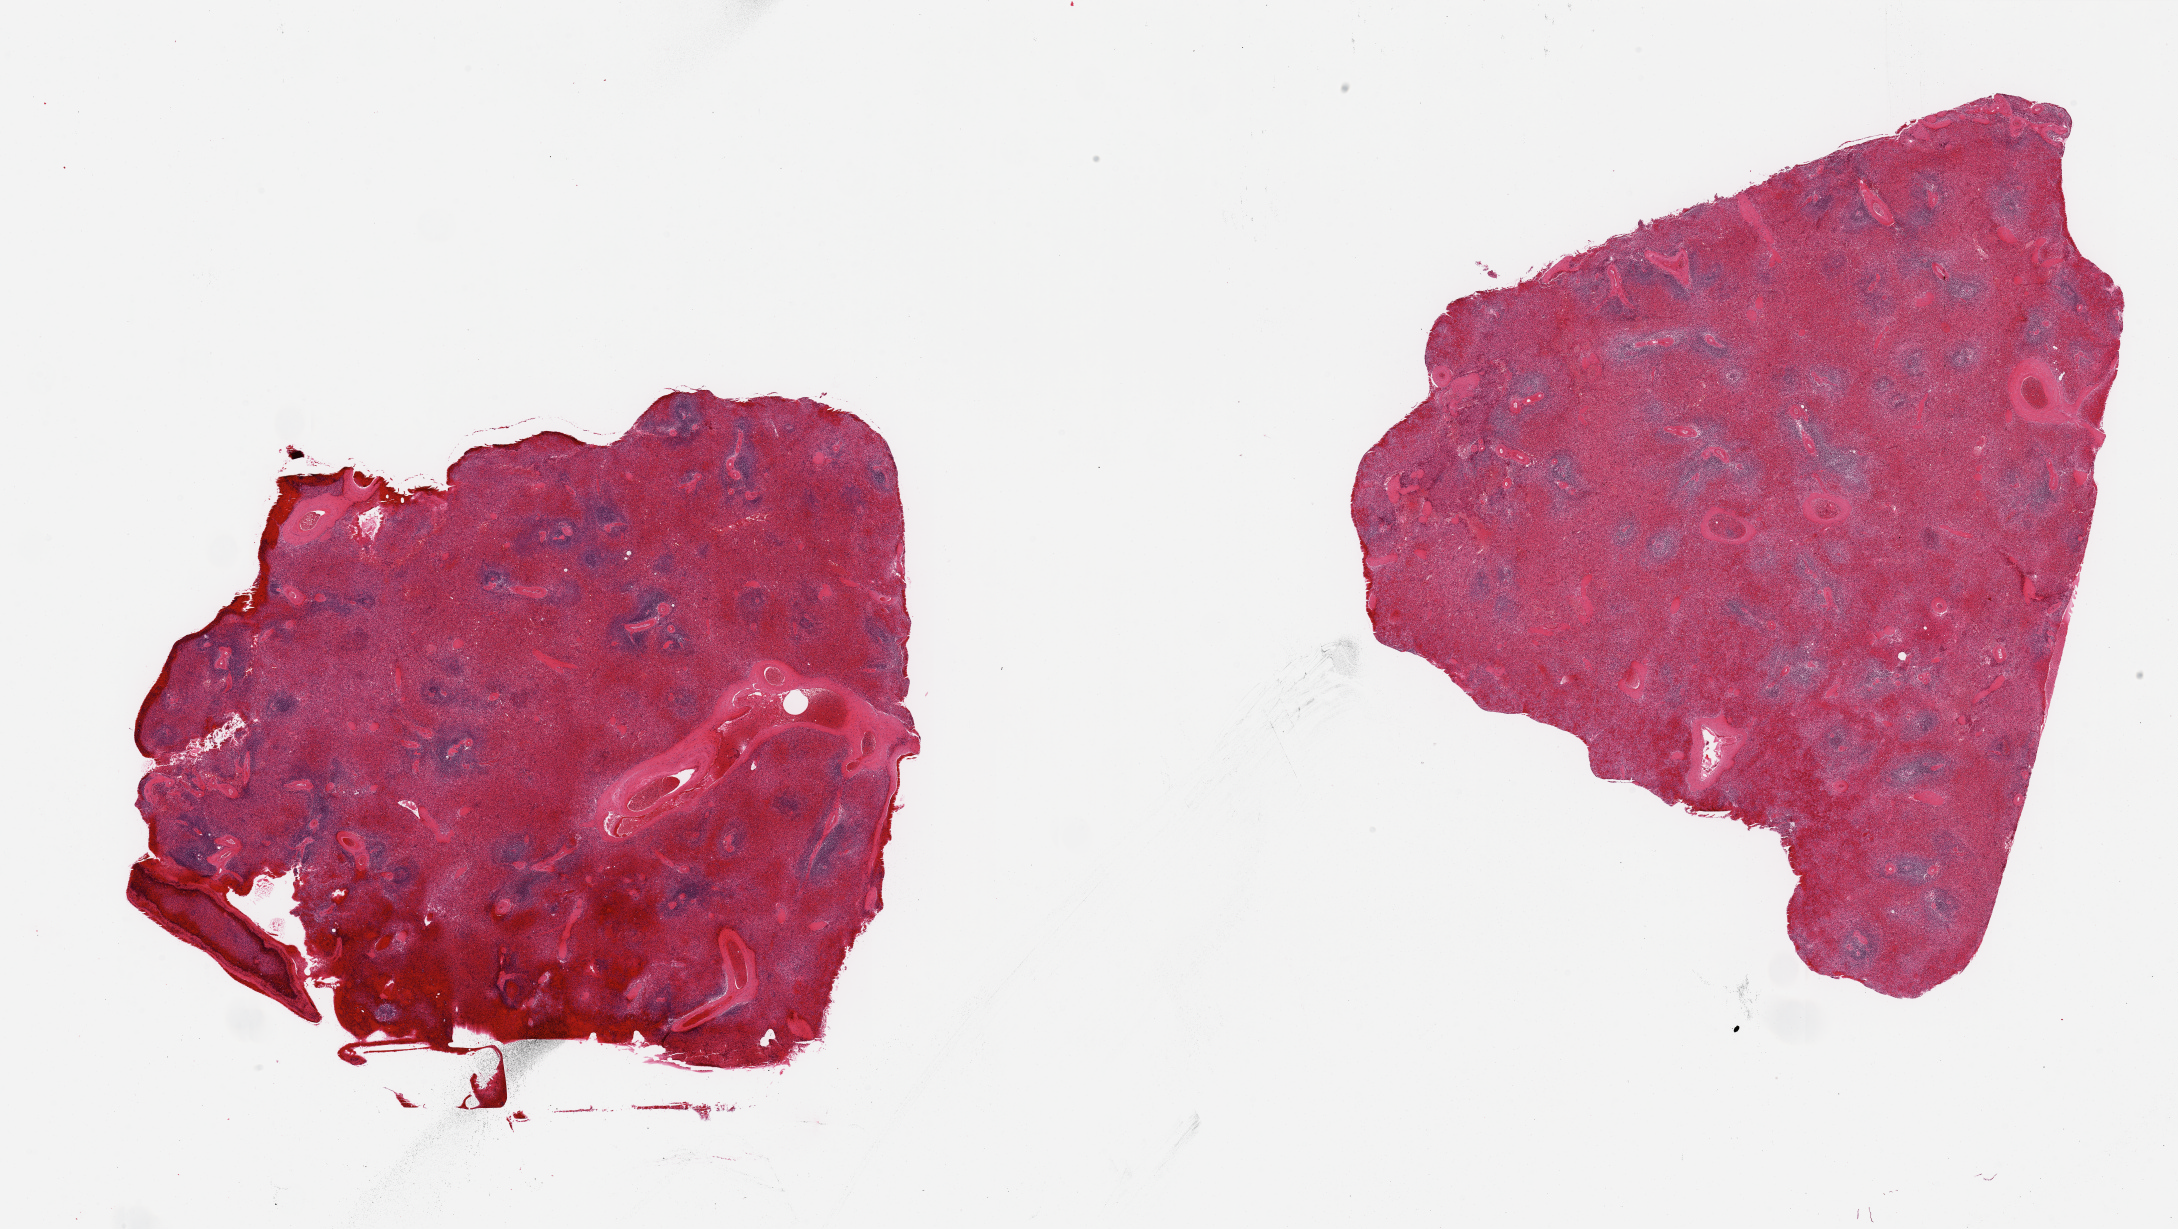
Digitized haematoxylin and eosin-stained section, brightfield, low-resolution overview of the scanned area, about 34.5 x 19.4 mm, PAXgene-fixed paraffin-embedded (PFPE) section, section of spleen (target tissue), donor tissue sample. Donor: female.
Reviewer comment on this tissue sample: 2 pieces; moderate to marked vascular congestion.